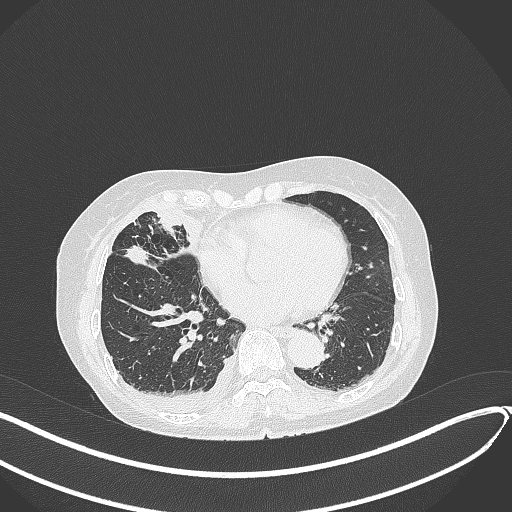
Chest CT, one axial slice. Slice 153 of 418 in the series (ordered by position). Reconstruction kernel B70f. 120 kVp. Lung window (W 1500 / L -600 HU). 1 mm slice thickness. 512 × 512 image matrix. Patient: female, 75 years. From the clinical record (not read from this slice): clinical TNM (as recorded): T2a N3 M0.
Structures marked on this image (bounding box drawn by a radiologist):
- lung tumour (recorded histology: adenocarcinoma): bounding box (x1, y1, x2, y2) in pixels: (119, 242, 155, 269)